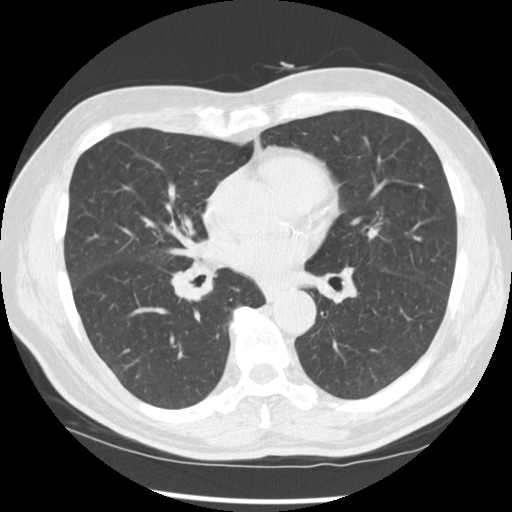
Low-dose screening chest CT, one axial slice. Position 140 of 277 along the scan axis. 120 kVp. Lung window (W 1500 / L -600 HU). 2.5 mm slice thickness. 512 × 512 image matrix, field of view 365 × 365 mm.
Annotated regions visible in this slice (expert manual segmentation):
- lesion 1 (tumor, middle lobe of right lung): bounding box [x1, y1, x2, y2] px = [171, 263, 212, 302]